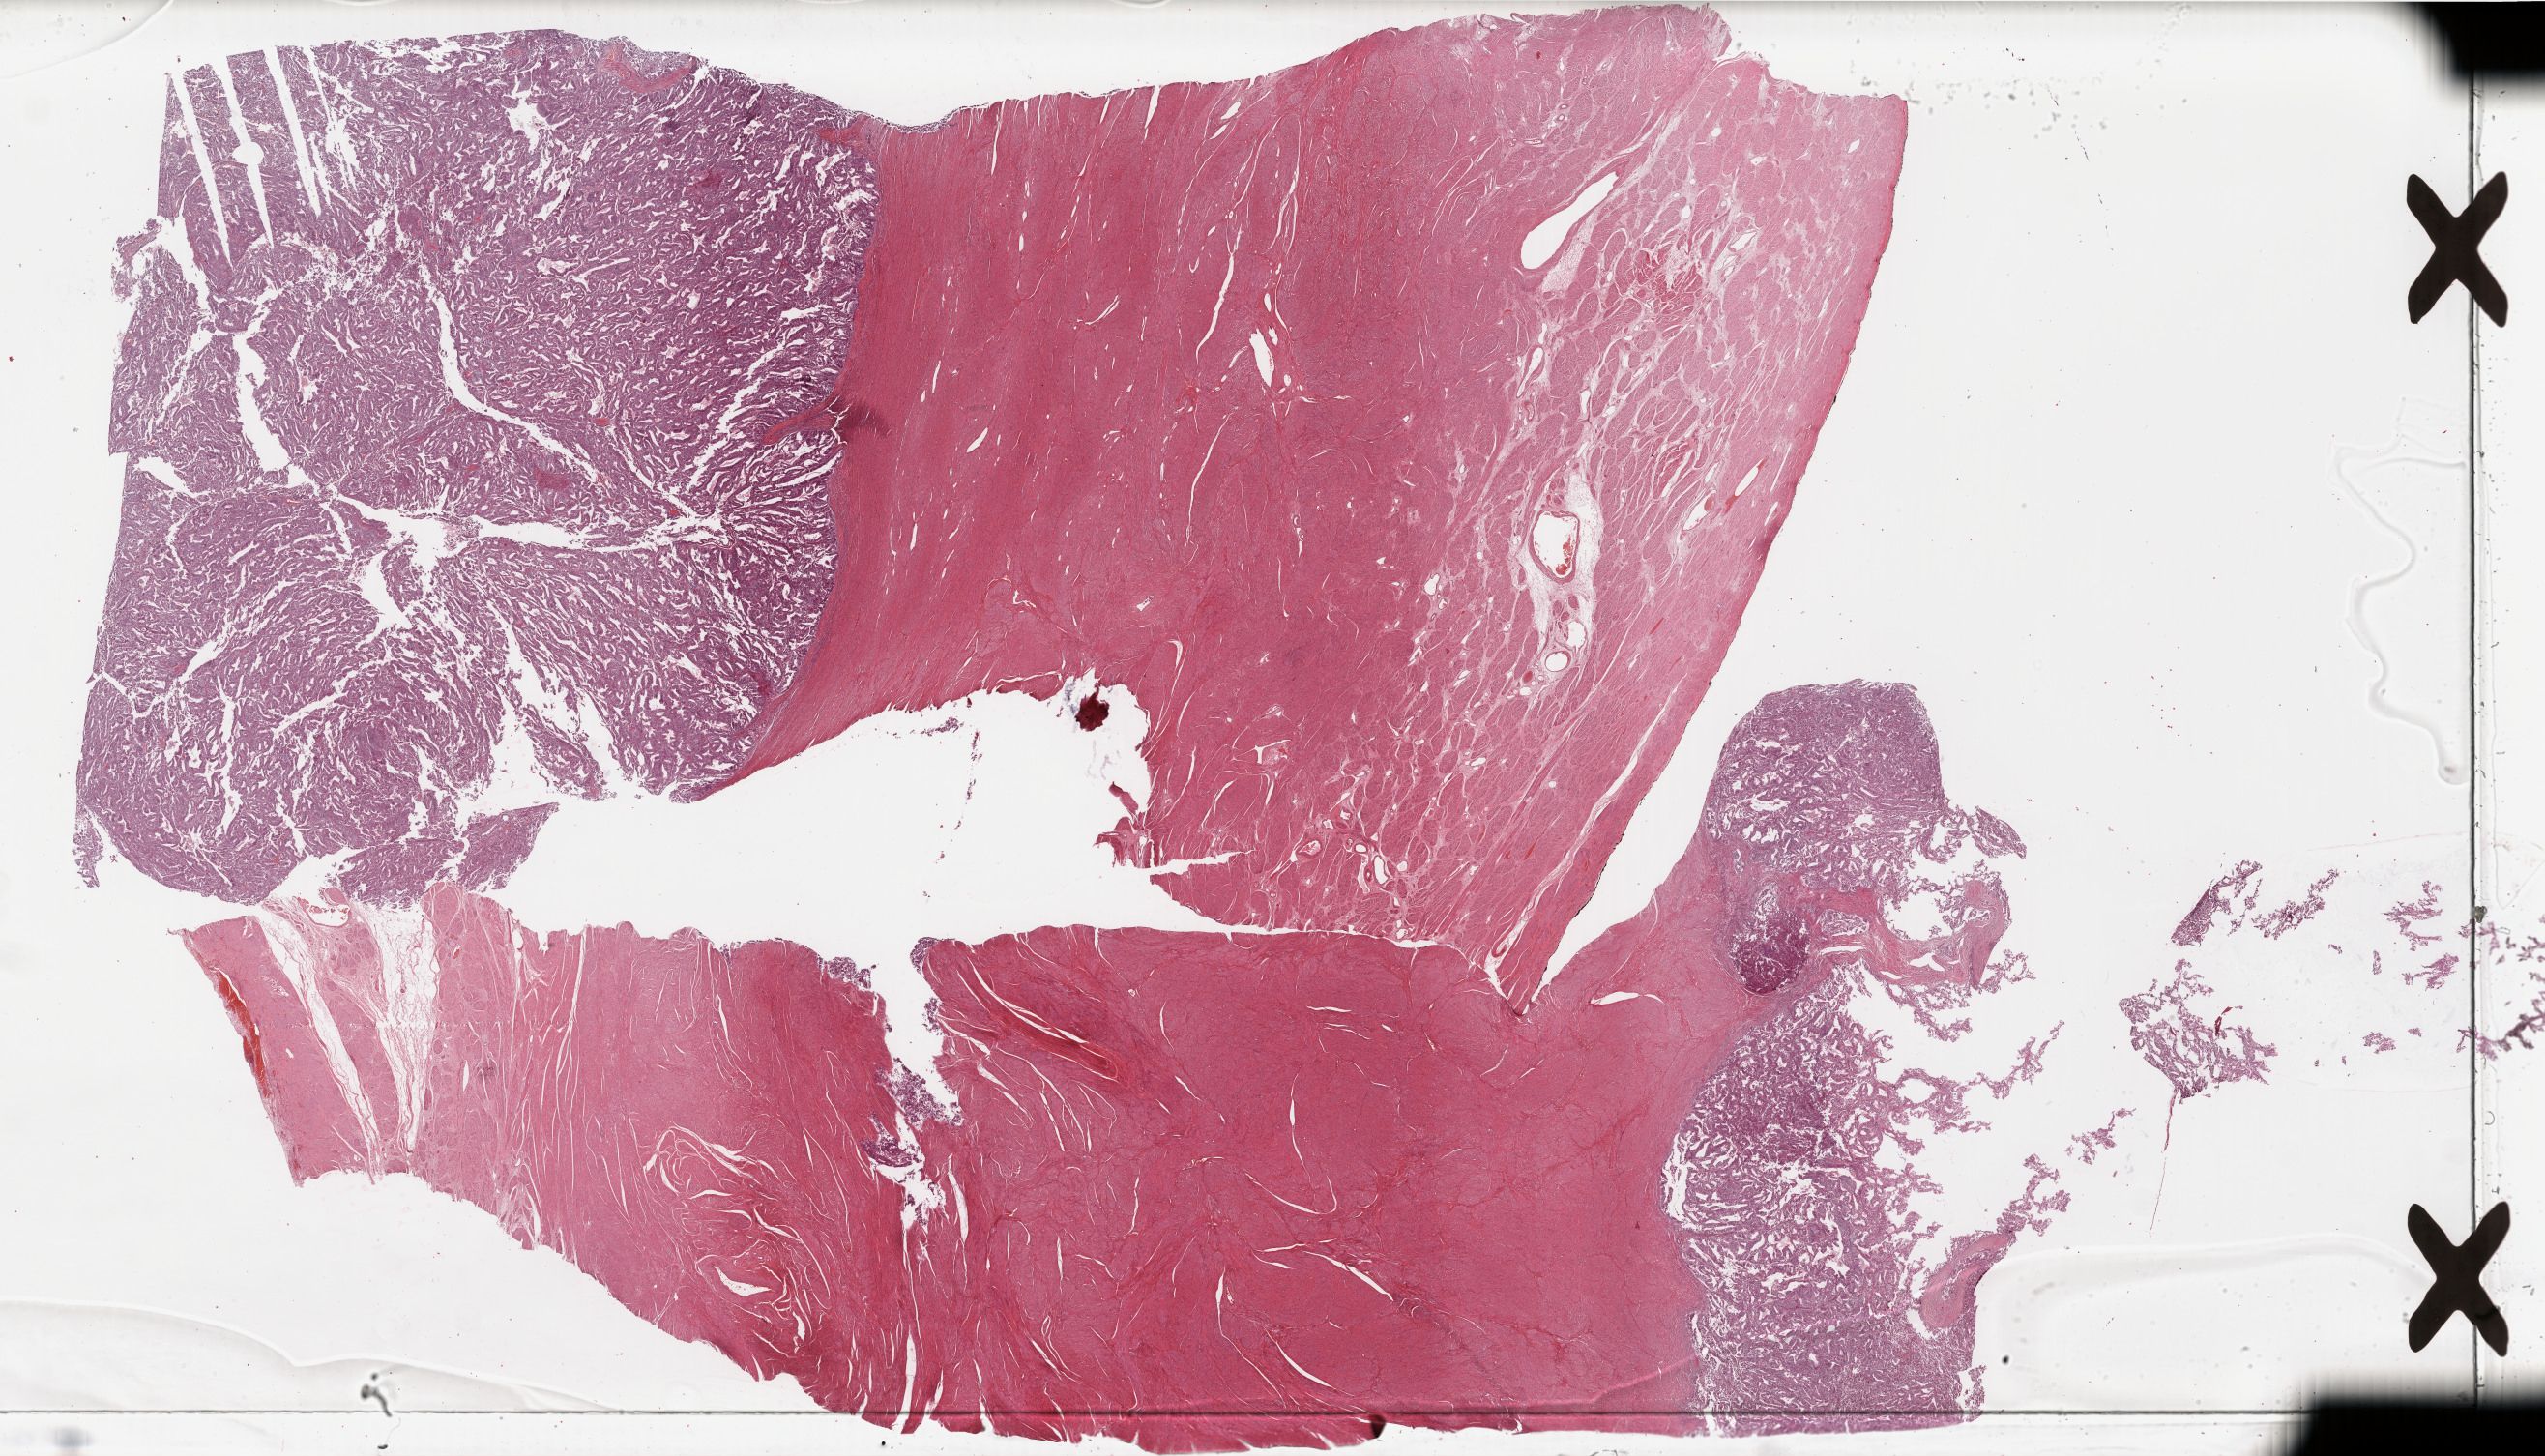
Whole-slide histology image, H&E, a low-resolution overview of the entire scanned area, about 41.8 x 23.9 mm (acquisition: 40x scan), FFPE section, sample: primary tumour, uterus. Patient: female, age at initial diagnosis 48 years. Histologic grade: G1 (well differentiated).
- FIGO stage: IB
- histologic diagnosis: Endometrioid adenocarcinoma, NOS (endometrium)
- lymph nodes positive (case pathology): 0 of 26 examined